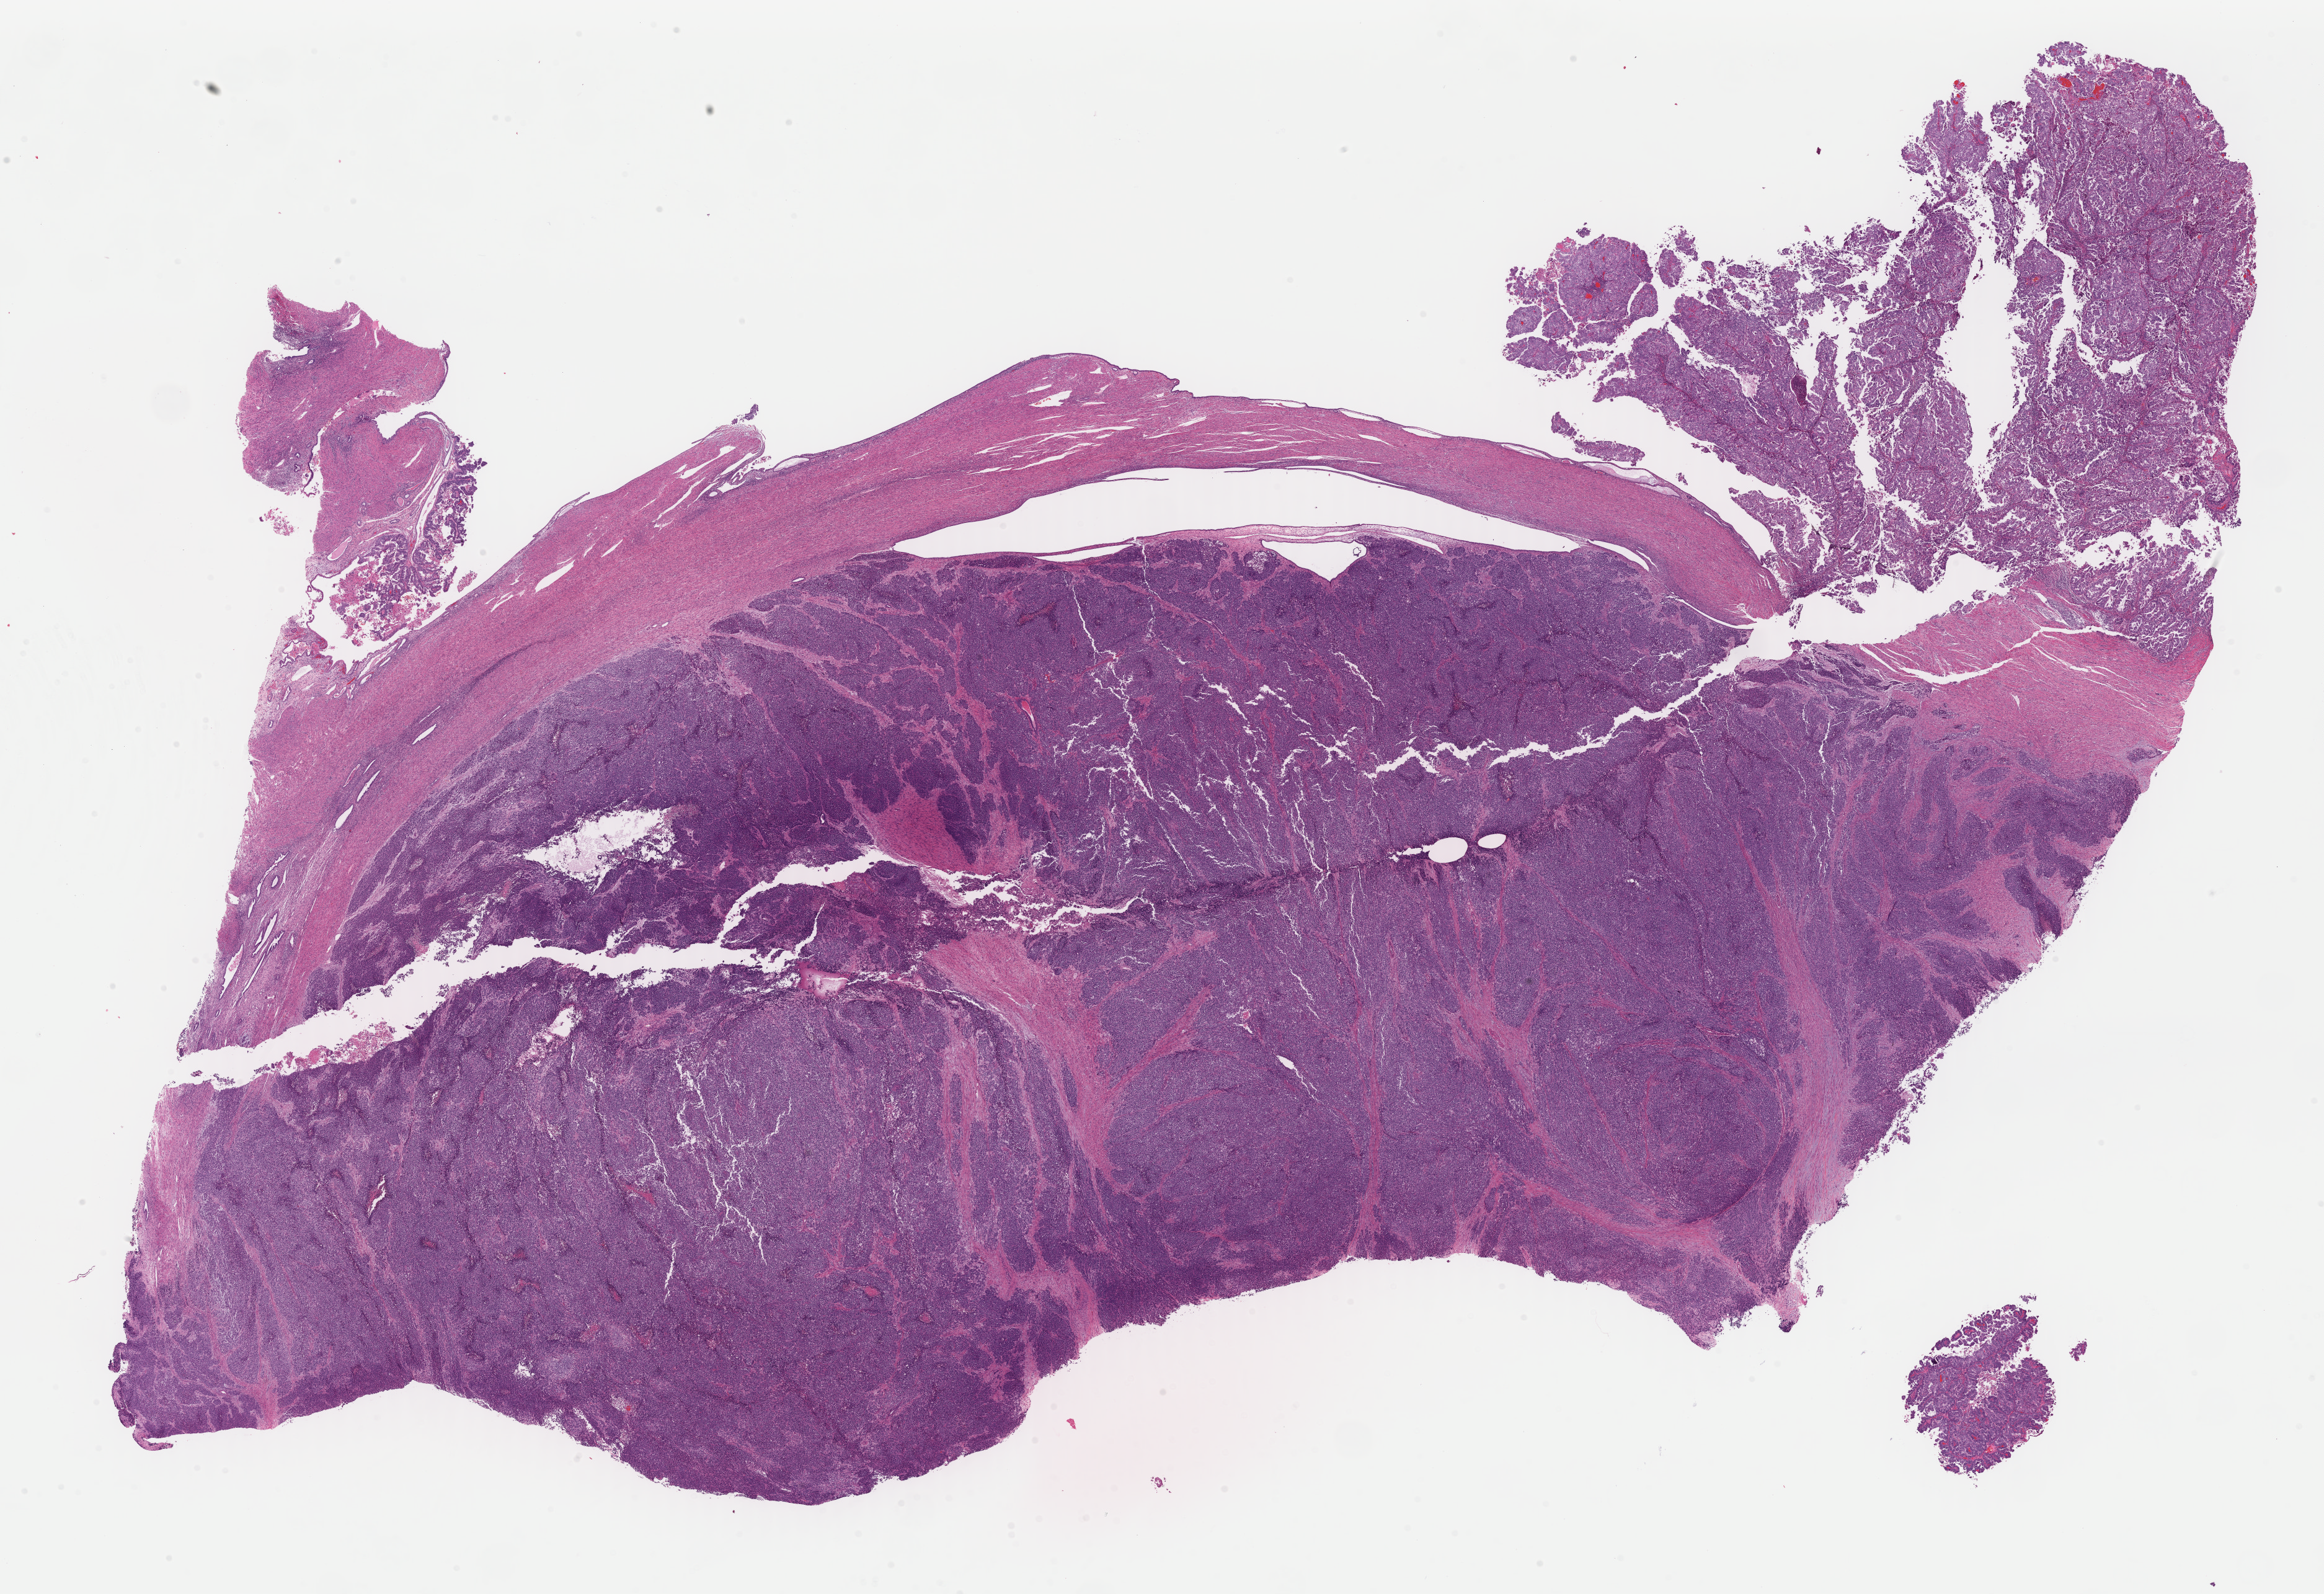
Whole-slide histology image, H&E, low-resolution overview of the scanned area, about 29.6 x 20.3 mm (acquisition: 40x scan); formalin-fixed paraffin-embedded (FFPE) diagnostic section; primary tumour sample from the uterus. Patient sex: female.
• FIGO stage: IC
• pathologic diagnosis: Mullerian mixed tumor (endometrium)